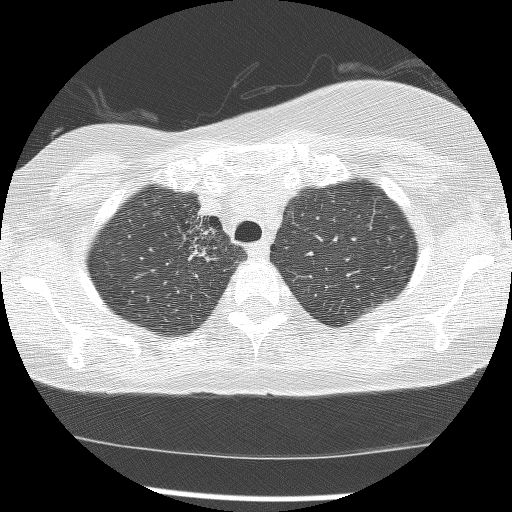
Axial slice from a low-dose chest CT screening exam, first (baseline) screen, lung window (W 1500 / L -600 HU), 2.5 mm slice thickness, 120 kVp, slice 32 of 172 in the series. Female, age 56 years at enrolment.
Expert reader's lesion annotation, bounding box (x1, y1, x2, y2) in pixels: (166, 208, 225, 277). The screening reader recorded 2 non-calcified nodules or masses ≥4 mm on this exam (right lower lobe, right middle lobe); which of them this box marks is not recorded. Later outcome: lung cancer diagnosed 1185 days after this screen — adenocarcinoma, NOS, right upper lobe, stage IIIB (AJCC 6th edition), 8 mm at pathology.